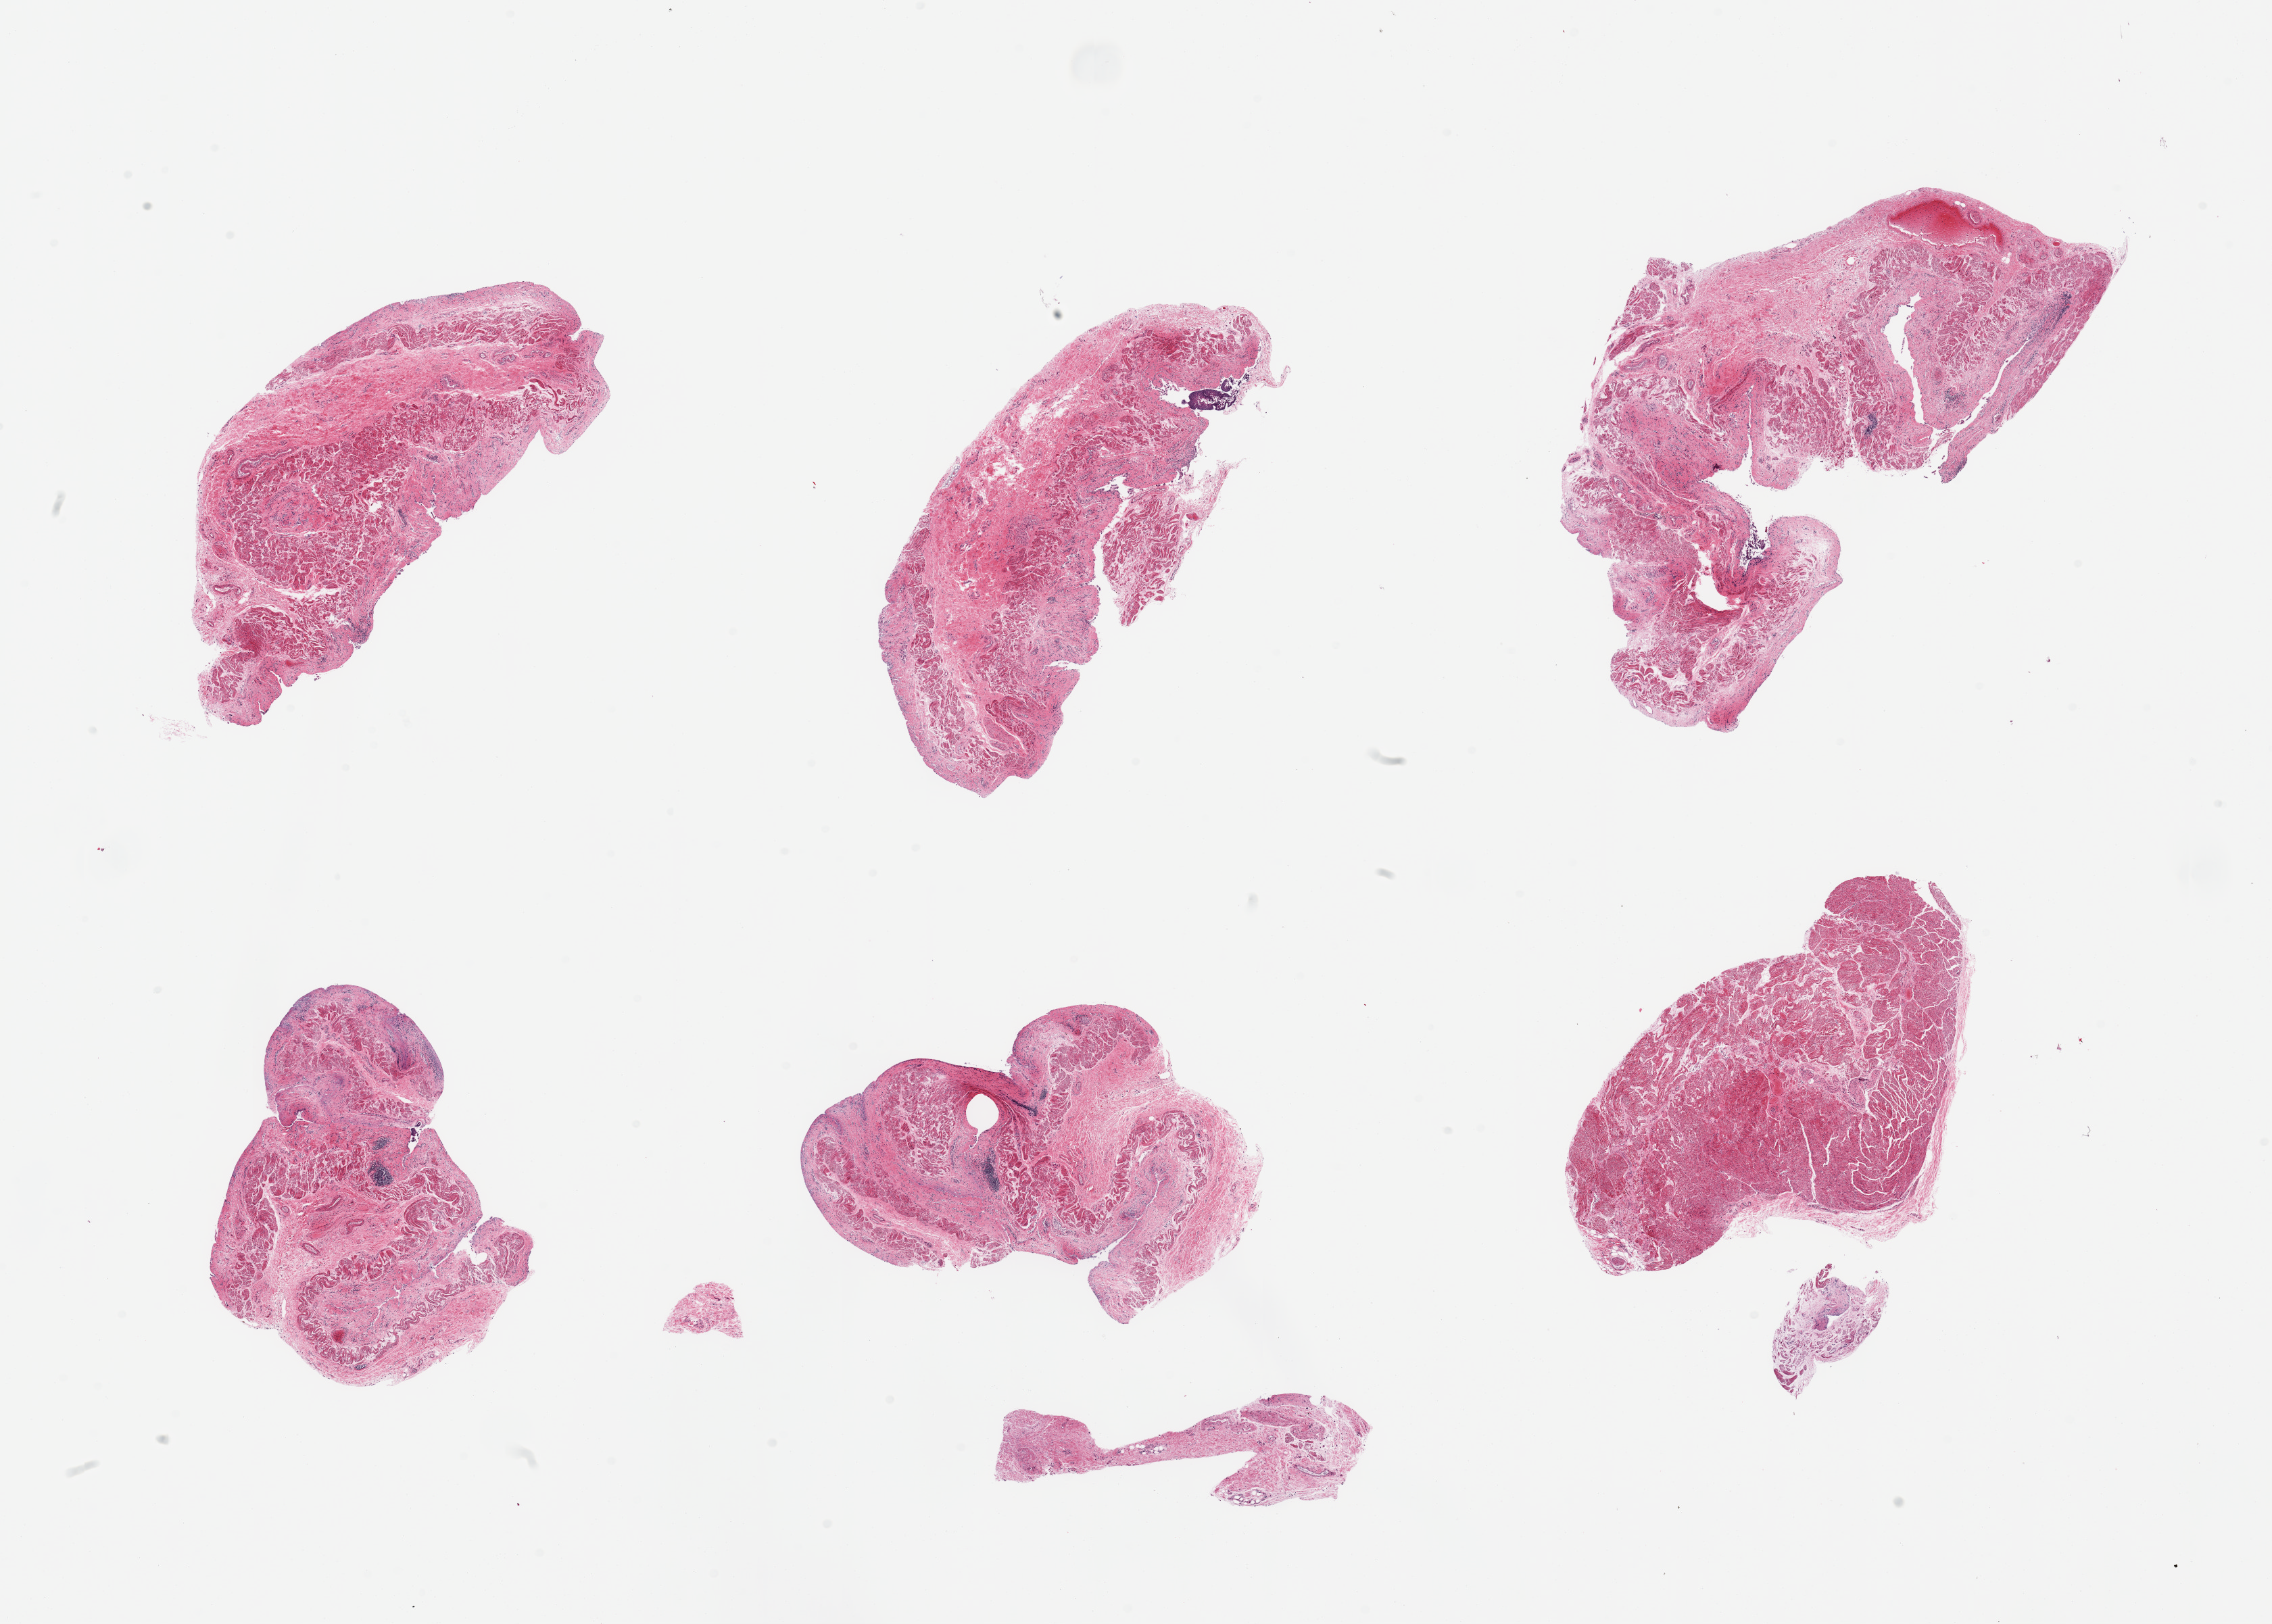
Digitized haematoxylin and eosin-stained section, brightfield — shown as a low-resolution overview of the whole scanned area (about 26.6 x 19.0 mm). PAXgene-fixed, paraffin-embedded tissue. Sampled site (target tissue): esophageal muscle. Donor tissue sample. Female donor.
Review note (as recorded): 6 pieces; some represent denuded mucosa, some muscularis.